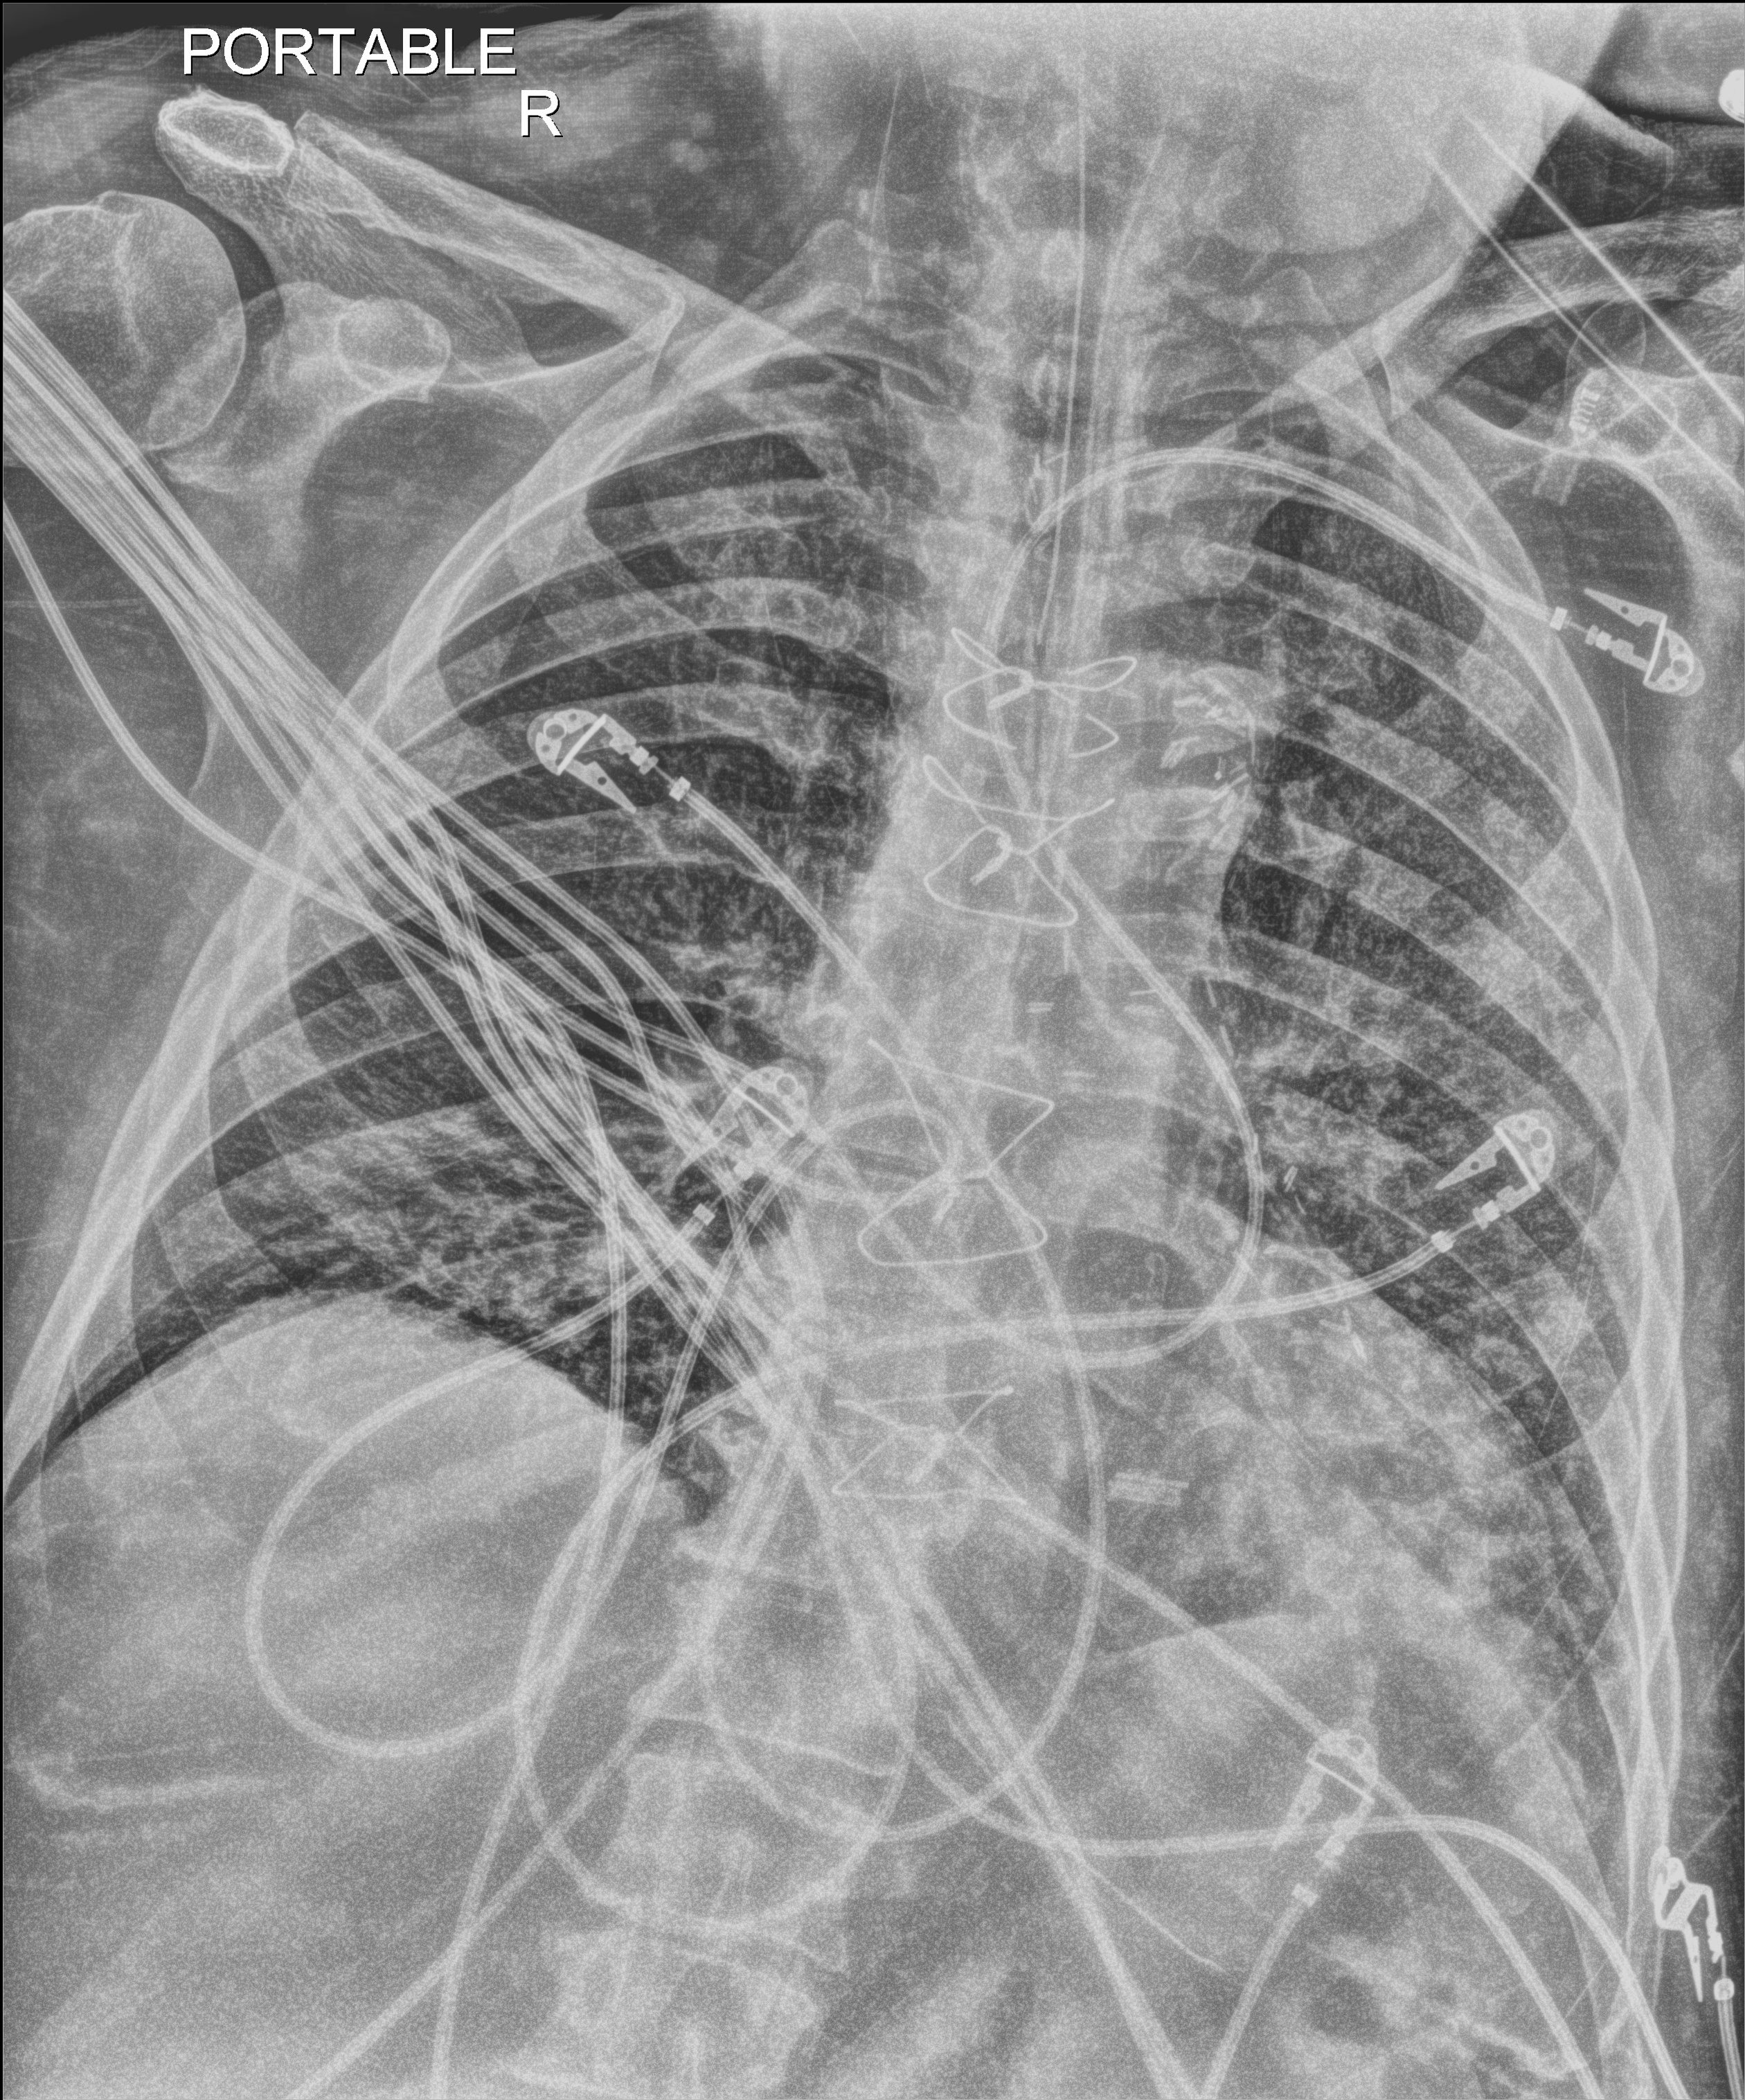
Portable chest radiograph; anteroposterior (AP) projection. Patient hospitalised with COVID-19; male, aged 60–74 years.
Admission-level facts for this patient (not findings on this image; timing relative to this image not recorded): mechanically ventilated during this hospital stay: yes; admitted to intensive care during this hospital stay: yes; diabetes (admission record): yes.